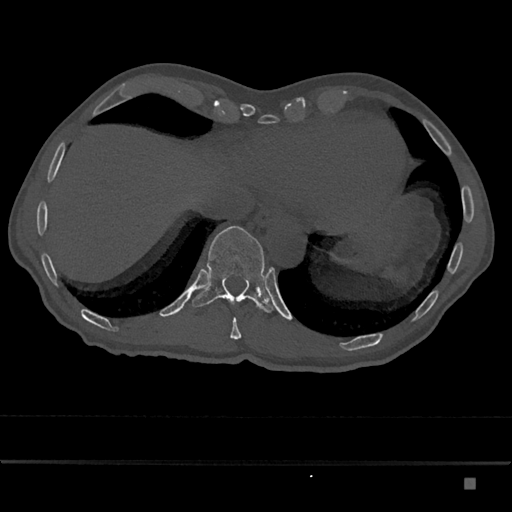
CT including the spine, one axial slice; position 696 of 797 along the scan axis; 120 kVp; bone window (W 1800 / L 400 HU); 0.5 mm slice thickness; 512 × 512 image matrix, field of view 390 × 390 mm. Patient: male, 72 years. From the clinical record (not read from this slice): primary cancer: prostate.
Outlined on this slice (semi-automatic segmentation, software-assisted and operator-edited):
- T10 vertebra: bounding box <230,318,242,339> (left, top, right, bottom; pixels)
- T11 vertebra: <192,226,274,313>